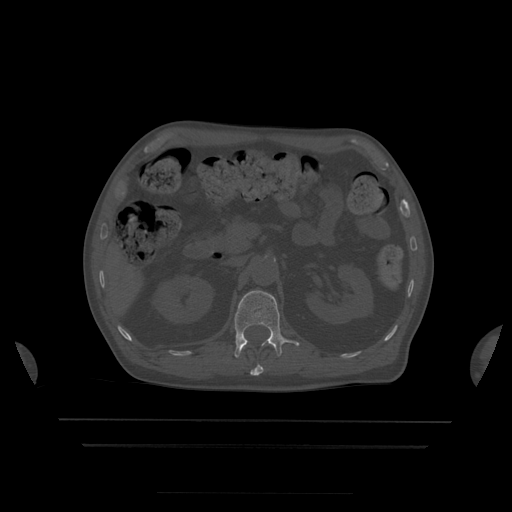
CT including the spine, one axial slice. Slice 177 of 522 in the series (ordered by position). Bone window (W 1800 / L 400 HU). 512 × 512 image matrix, field of view 436 × 436 mm. Patient age 68 years. From the clinical record (not read from this slice): primary cancer: urothelial.
Structures marked on this image (semi-automatically segmented with operator editing):
- L1 vertebra: bounding box (x1, y1, x2, y2) in pixels: (234, 291, 300, 358)
- T12 vertebra: (250, 365, 264, 376)